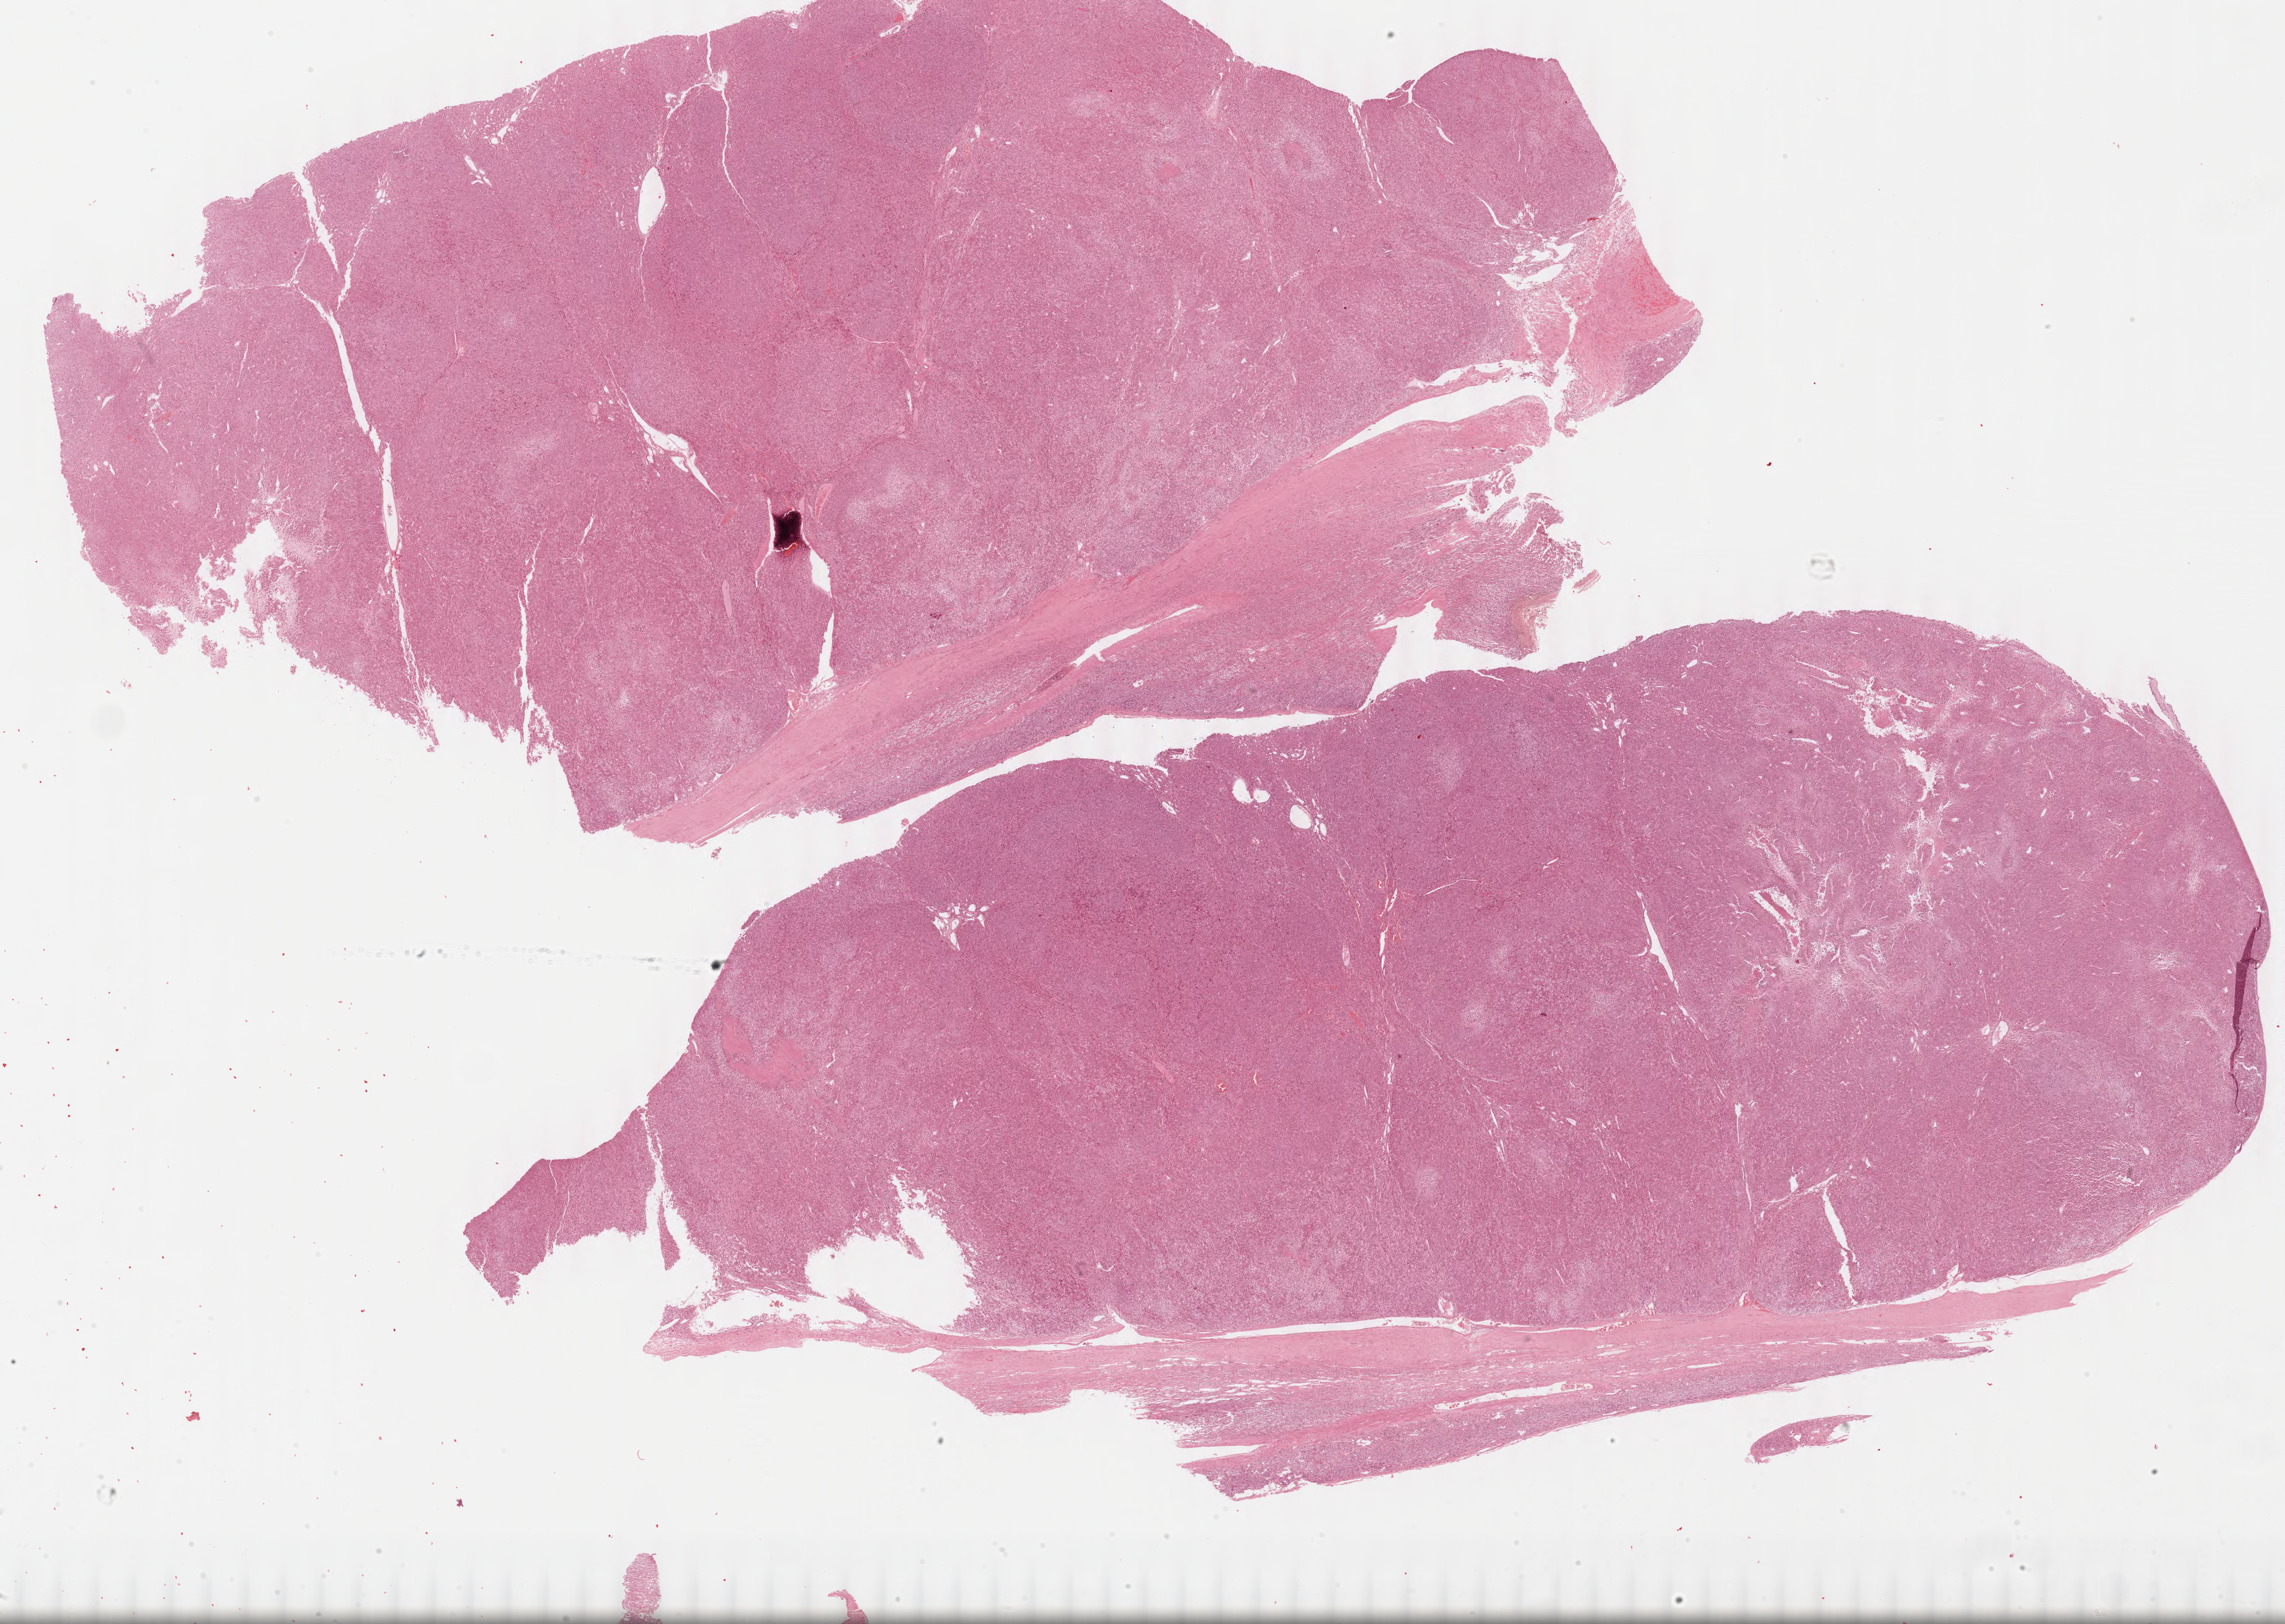
Whole-slide histology image, H&E — whole scanned area (about 30.0 x 21.3 mm, slide scanned at 40x) shown as a low-resolution overview; formalin-fixed paraffin-embedded (FFPE) diagnostic section; sample: primary tumour, adrenal cortex. Patient: male, age at initial diagnosis 42 years.
• pathologic diagnosis: Adrenal cortical carcinoma (cortex of adrenal gland)
• laterality: right